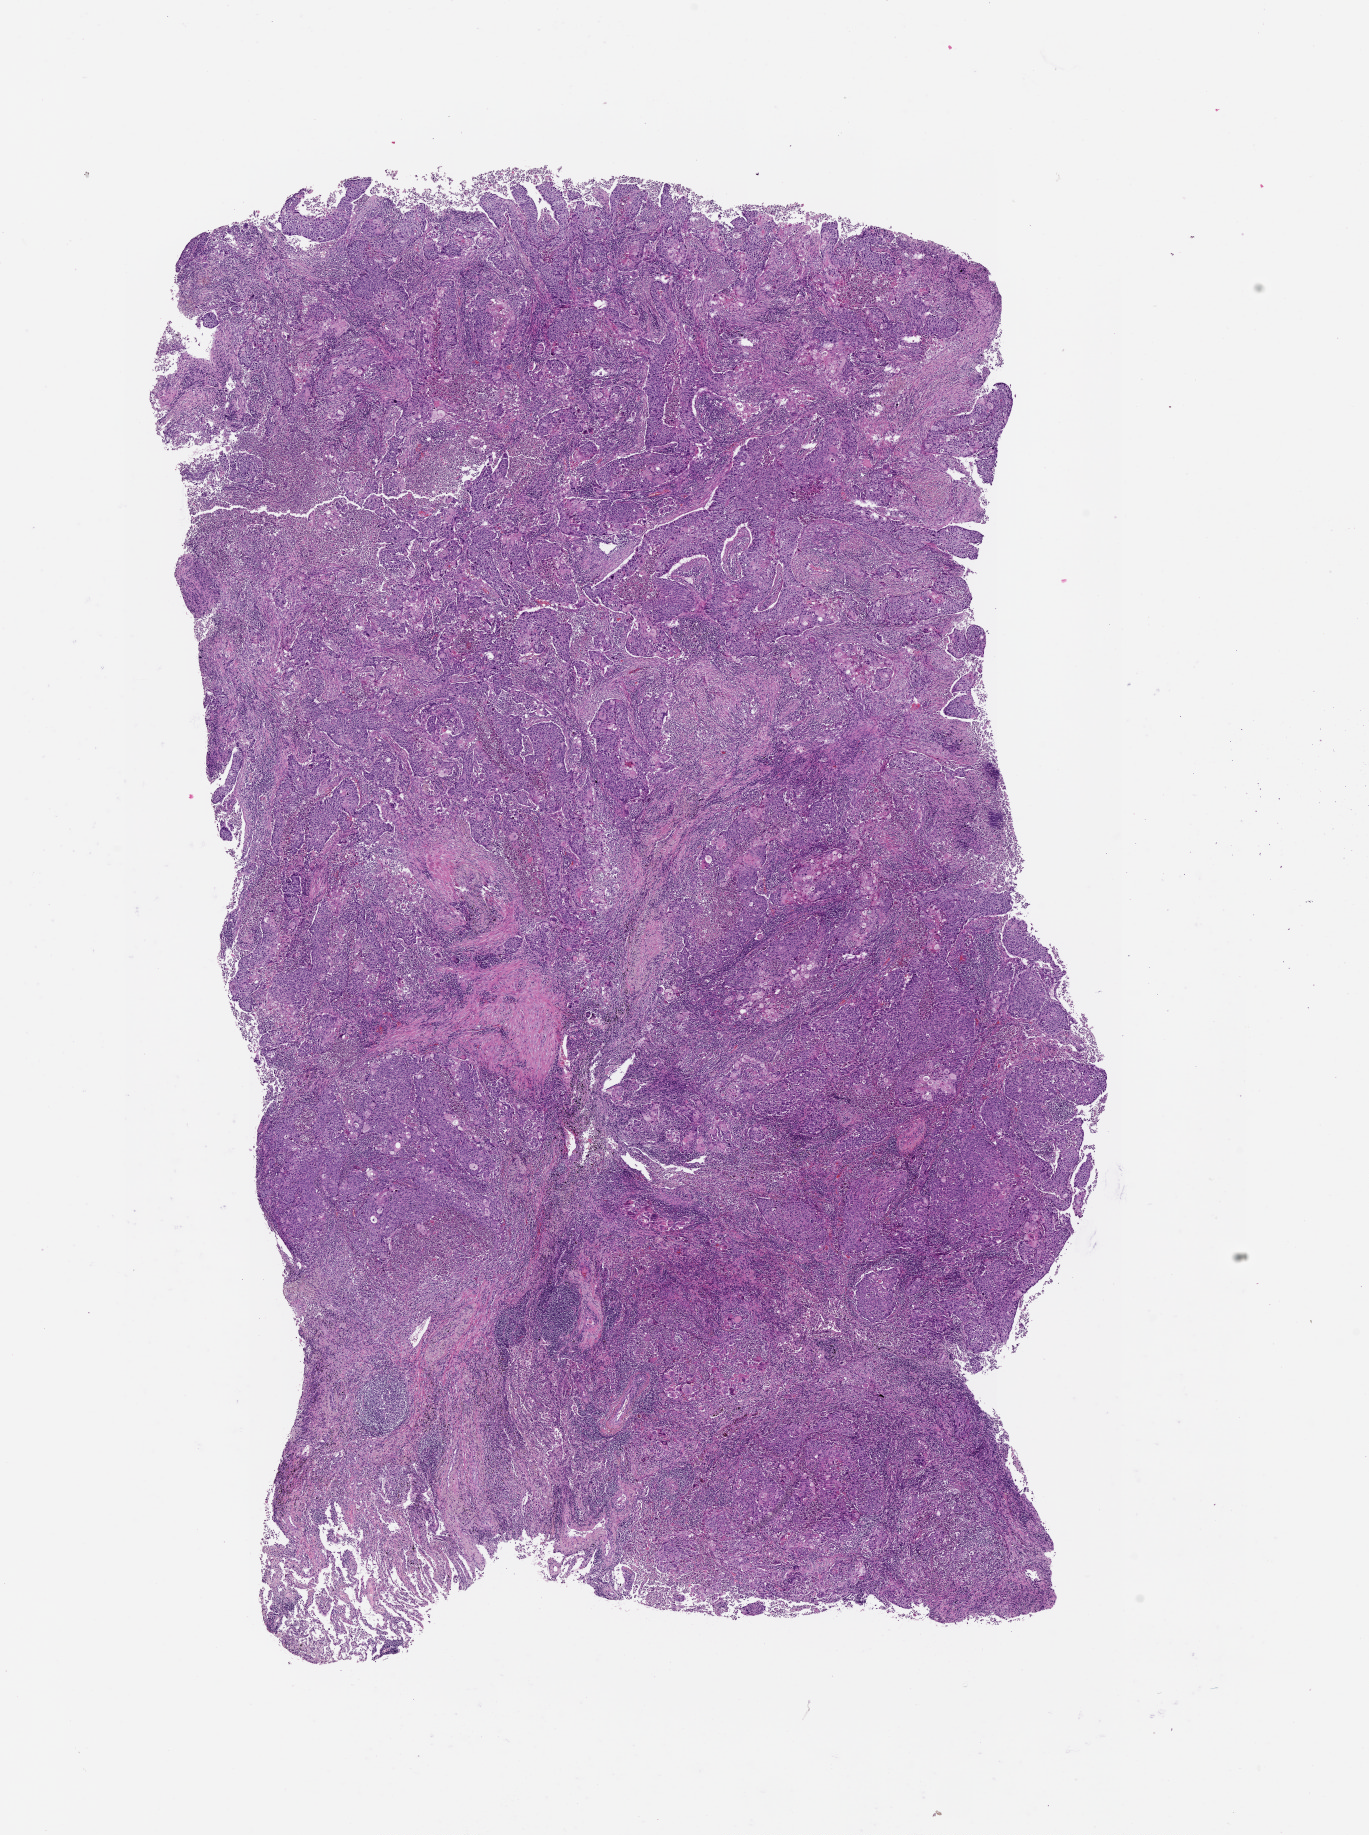
Hematoxylin and eosin (H&E) stained whole-slide image — low-resolution overview of the scanned area, about 11.0 x 14.8 mm, tumour tissue sample, lung. Male, 64 y/o.
Patient diagnosis (cohort enrolment): squamous cell carcinoma (lung).